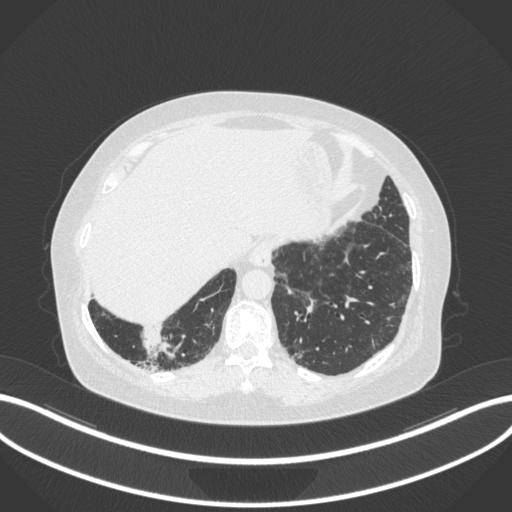
Chest CT, one axial slice; position 20 of 303 along the scan axis; lung window (W 1500 / L -600 HU); 512 × 512 image matrix. Patient: female, 65 years. From the clinical record (not read from this slice): clinical TNM (as recorded): T2b N1 M0.
Structures marked on this image (rectangle marked by the reading radiologist):
- lung tumour (recorded histology: adenocarcinoma): bounding box [x1, y1, x2, y2] px = [136, 327, 175, 360]